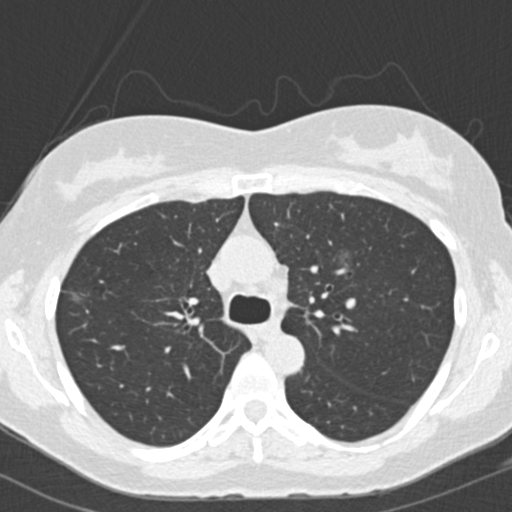
Low-dose screening chest CT, one axial slice. Position 112 of 157 along the scan axis. Reconstruction kernel B30f. 120 kVp. Lung window (W 1500 / L -600 HU). 2 mm slice thickness. 512 × 512 image matrix, field of view 290 × 290 mm.
Structures marked on this image (outlined manually by an expert reader):
- lesion 1 (tumor, upper lobe of right lung): bounding box (x1, y1, x2, y2) in pixels: (70, 292, 81, 302)